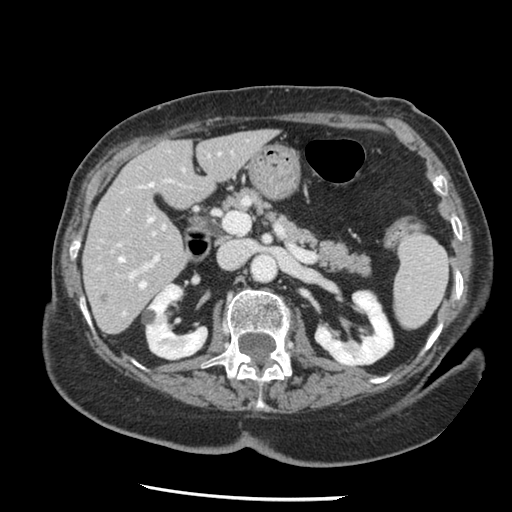
Contrast-enhanced abdominal CT, one axial slice. Position 68 of 148 along the scan axis. Reconstruction kernel STANDARD. 120 kVp. Soft-tissue window (W 400 / L 40 HU). 512 × 512 image matrix. Female patient, age 85 years. From the clinical record (not read from this slice): diagnosis: colorectal cancer liver metastases, imaged before liver resection; multiple liver metastases: no; largest metastasis: 0.9 cm; disease in both lobes: no.
Outlined on this slice (manually delineated by an expert):
- hepatic veins: bounding box <119,219,152,288> (left, top, right, bottom; pixels)
- liver: <84,131,275,333>
- planned liver remnant (the part of the liver to remain after resection): <84,131,275,330>
- portal vein (with intrahepatic branches): <117,209,160,281>
- liver metastasis: <101,293,109,302>